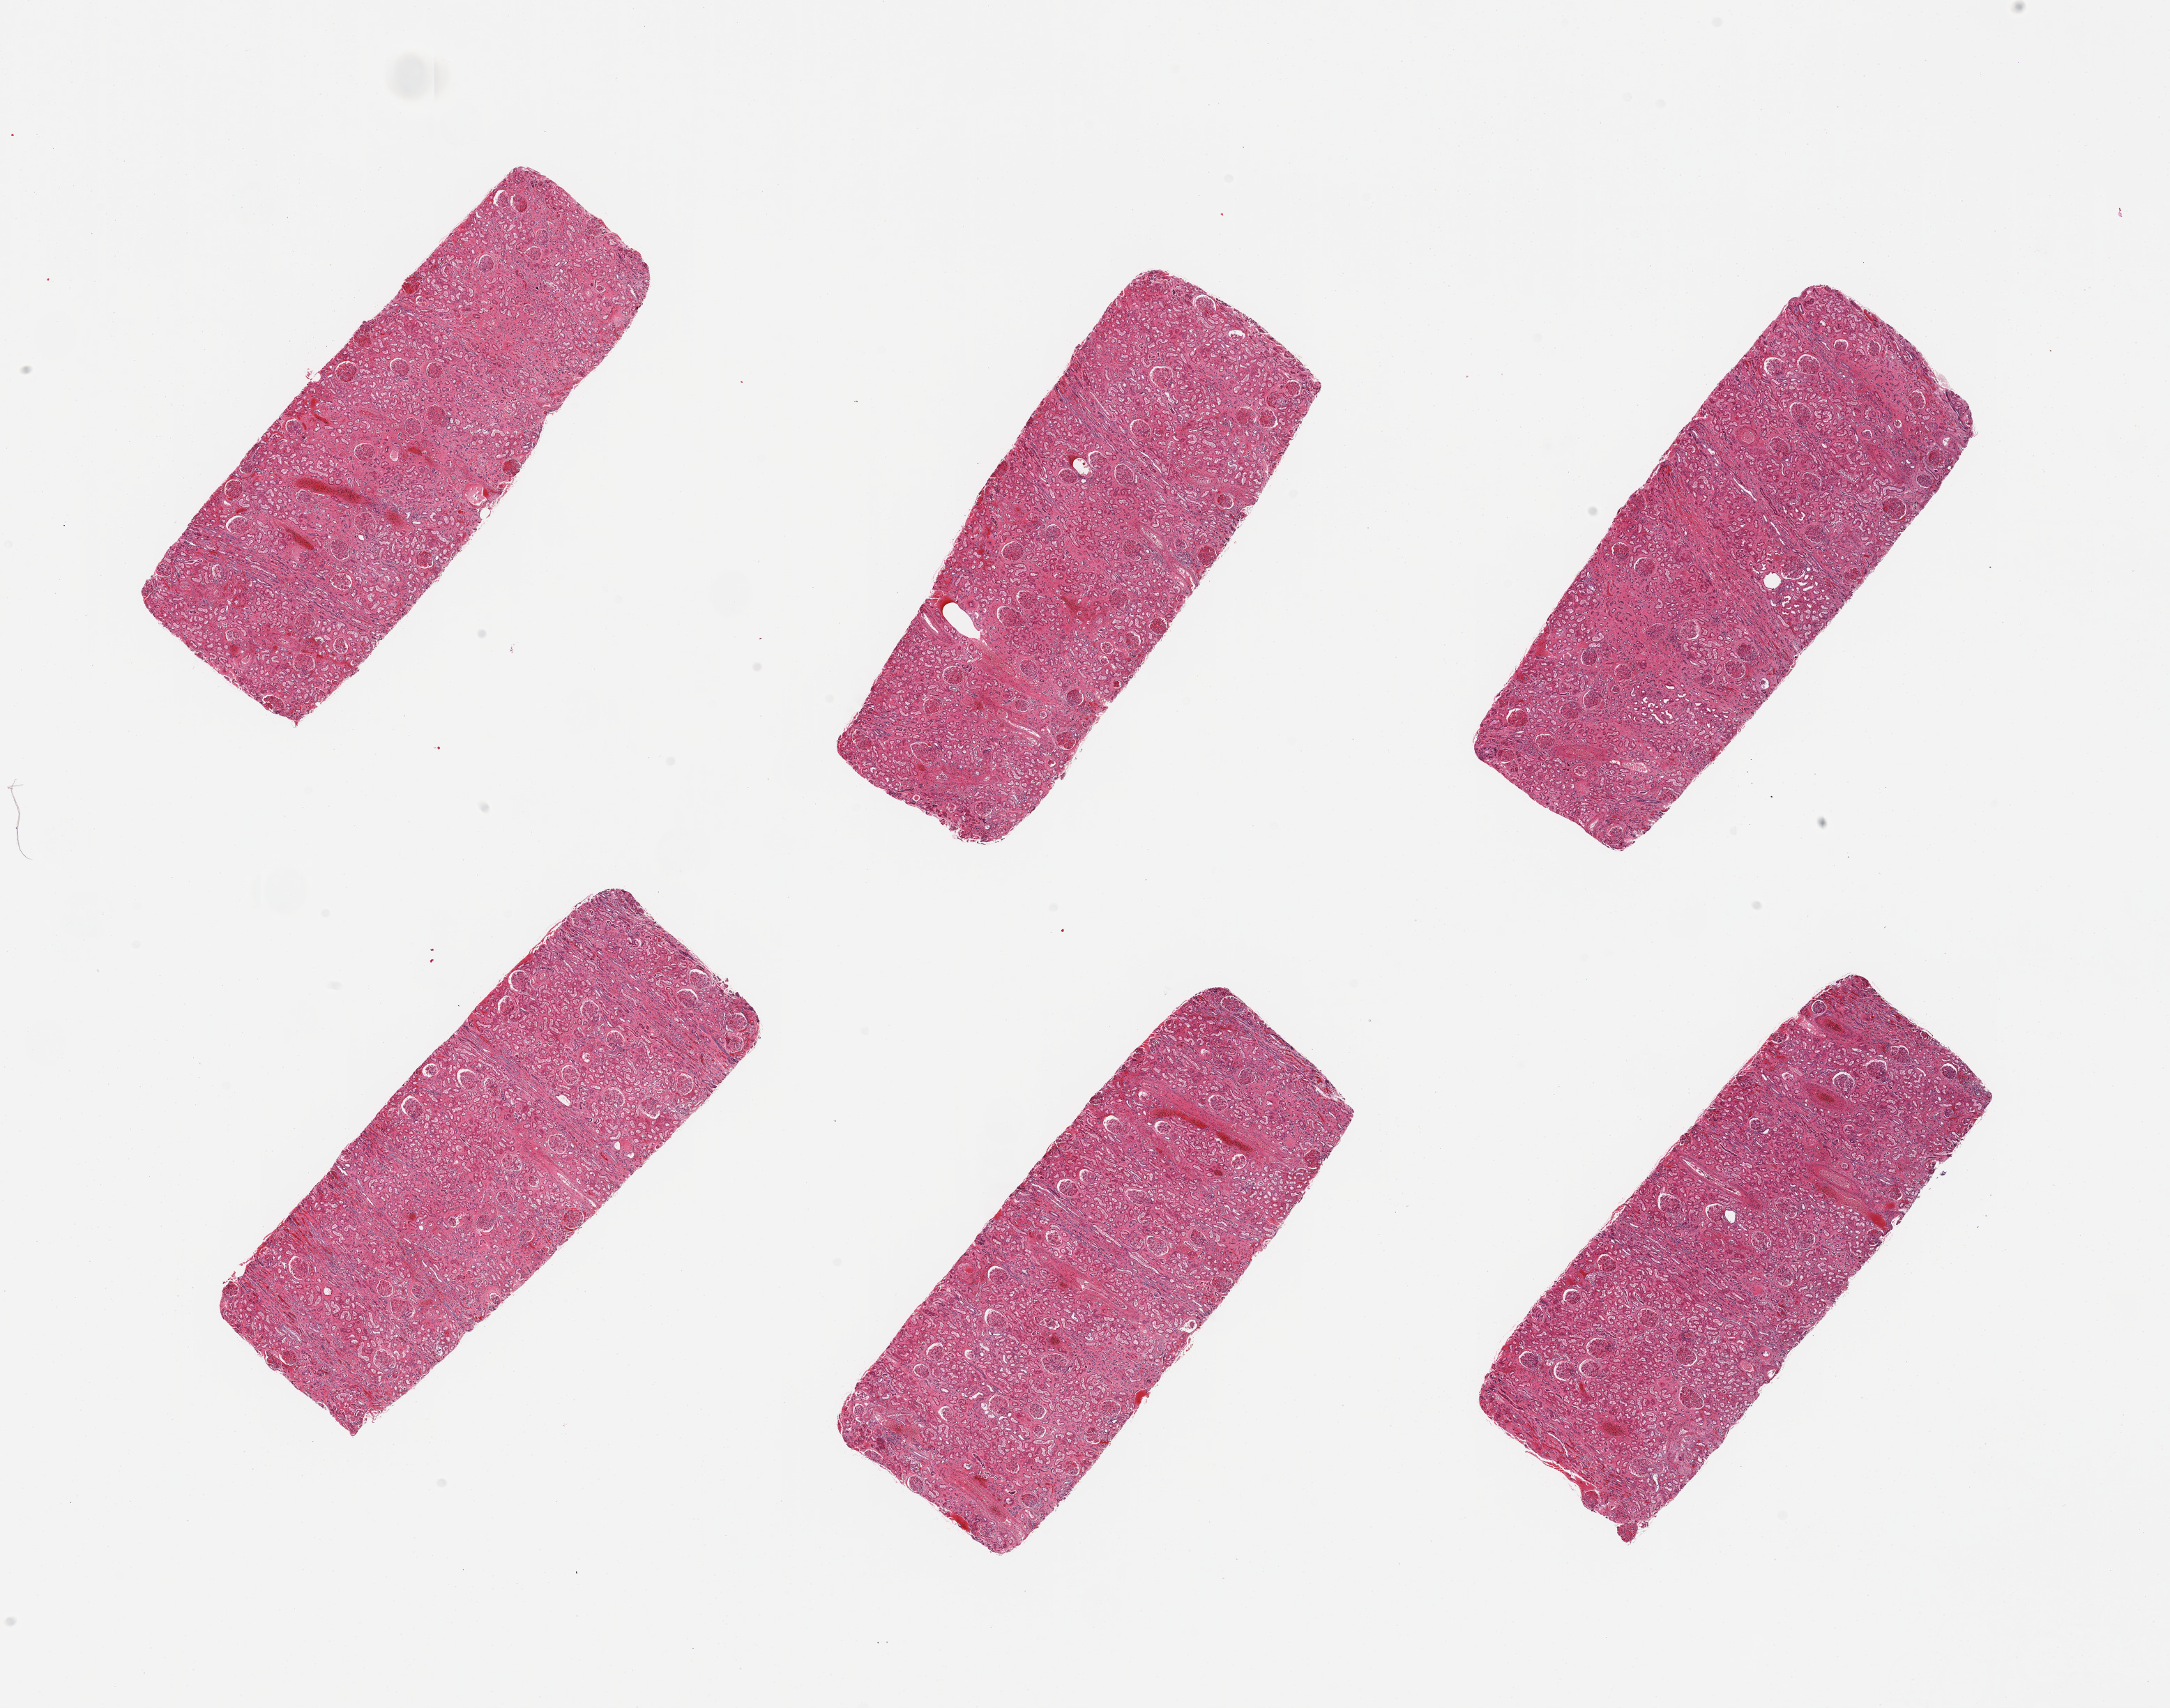
Digitized hematoxylin and eosin (H&E)-stained section, brightfield, a low-resolution overview of the entire scanned area, about 24.6 x 19.4 mm (from a 20x scan). PAXgene-fixed, paraffin-embedded tissue. Section of renal cortex (target tissue). Tissue donor sample.
- reviewer comment on this tissue sample: 6 pieces; glomeruli in all sections, increased mesangial matirx and rare sclerotic glomerulus, some vascular thickening, interstitial and periglomerular fibrosis